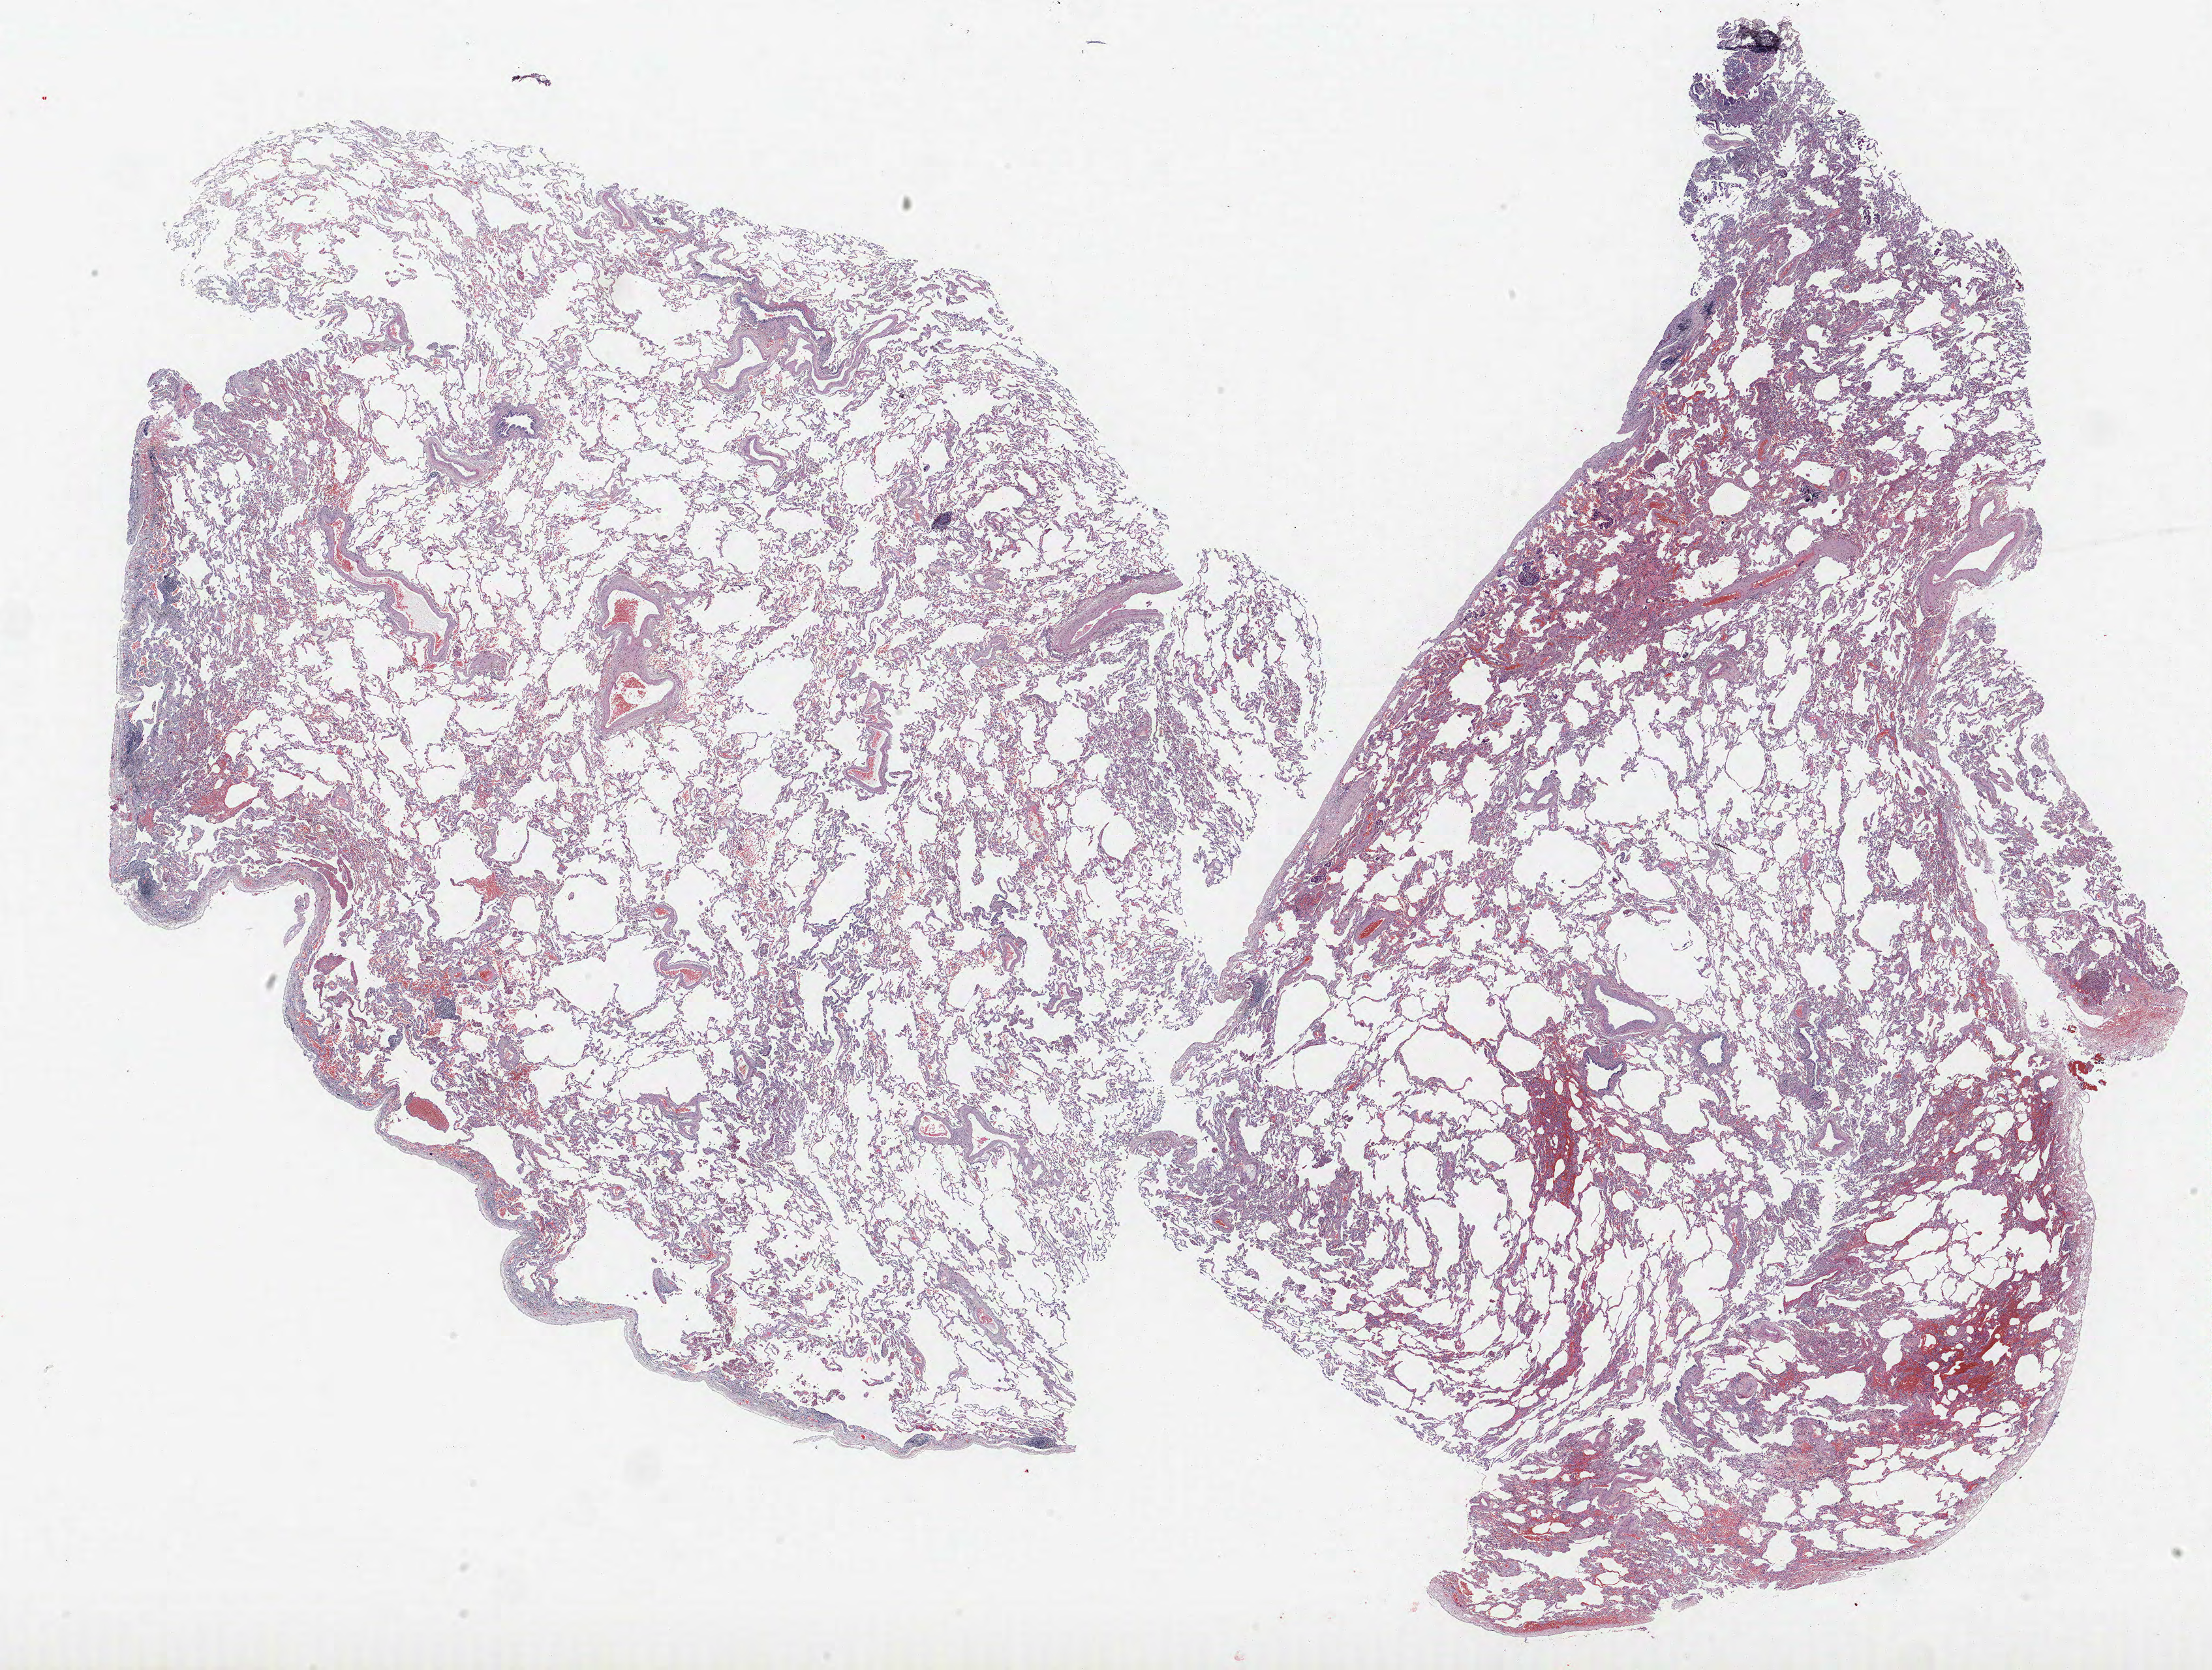
Whole-slide histology image, Hematoxylin and eosin (H&E) stained, a low-resolution overview of the entire scanned area, about 27.1 x 20.5 mm (acquisition: 40x scan), formalin-fixed paraffin-embedded (FFPE) section, lung. Female, age 63 at enrolment. Grade: well differentiated (G1).
* ICD-O-3 topography: upper lobe of lung (C34.1)
* stage (AJCC 6th edition): IA
* primary tumour location (clinical record): right upper lobe
* tumour size (pathology): 90 mm
* participant's lung-cancer diagnosis: Adenocarcinoma, NOS (ICD-O-3 8140/3)